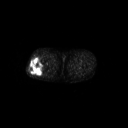
FDG PET of an extremity soft-tissue mass (from a PET/CT study), one axial slice. Slice 252 of 267 in the series (ordered by position). 128 × 128 image matrix, field of view 700 × 700 mm. Male patient, age 43 years. Case-level facts recorded for this patient, not image findings: histological type: poorly differentiated synovial sarcoma; grade: high; site of the primary tumour: right buttock.
Outlined on this slice (expert contour drawn on MRI and transferred to this co-registered scan by the dataset authors):
- gross tumour volume including surrounding oedema: bounding box (x1, y1, x2, y2) in pixels: (29, 57, 45, 76)
- gross tumour volume (mass): (29, 57, 44, 76)